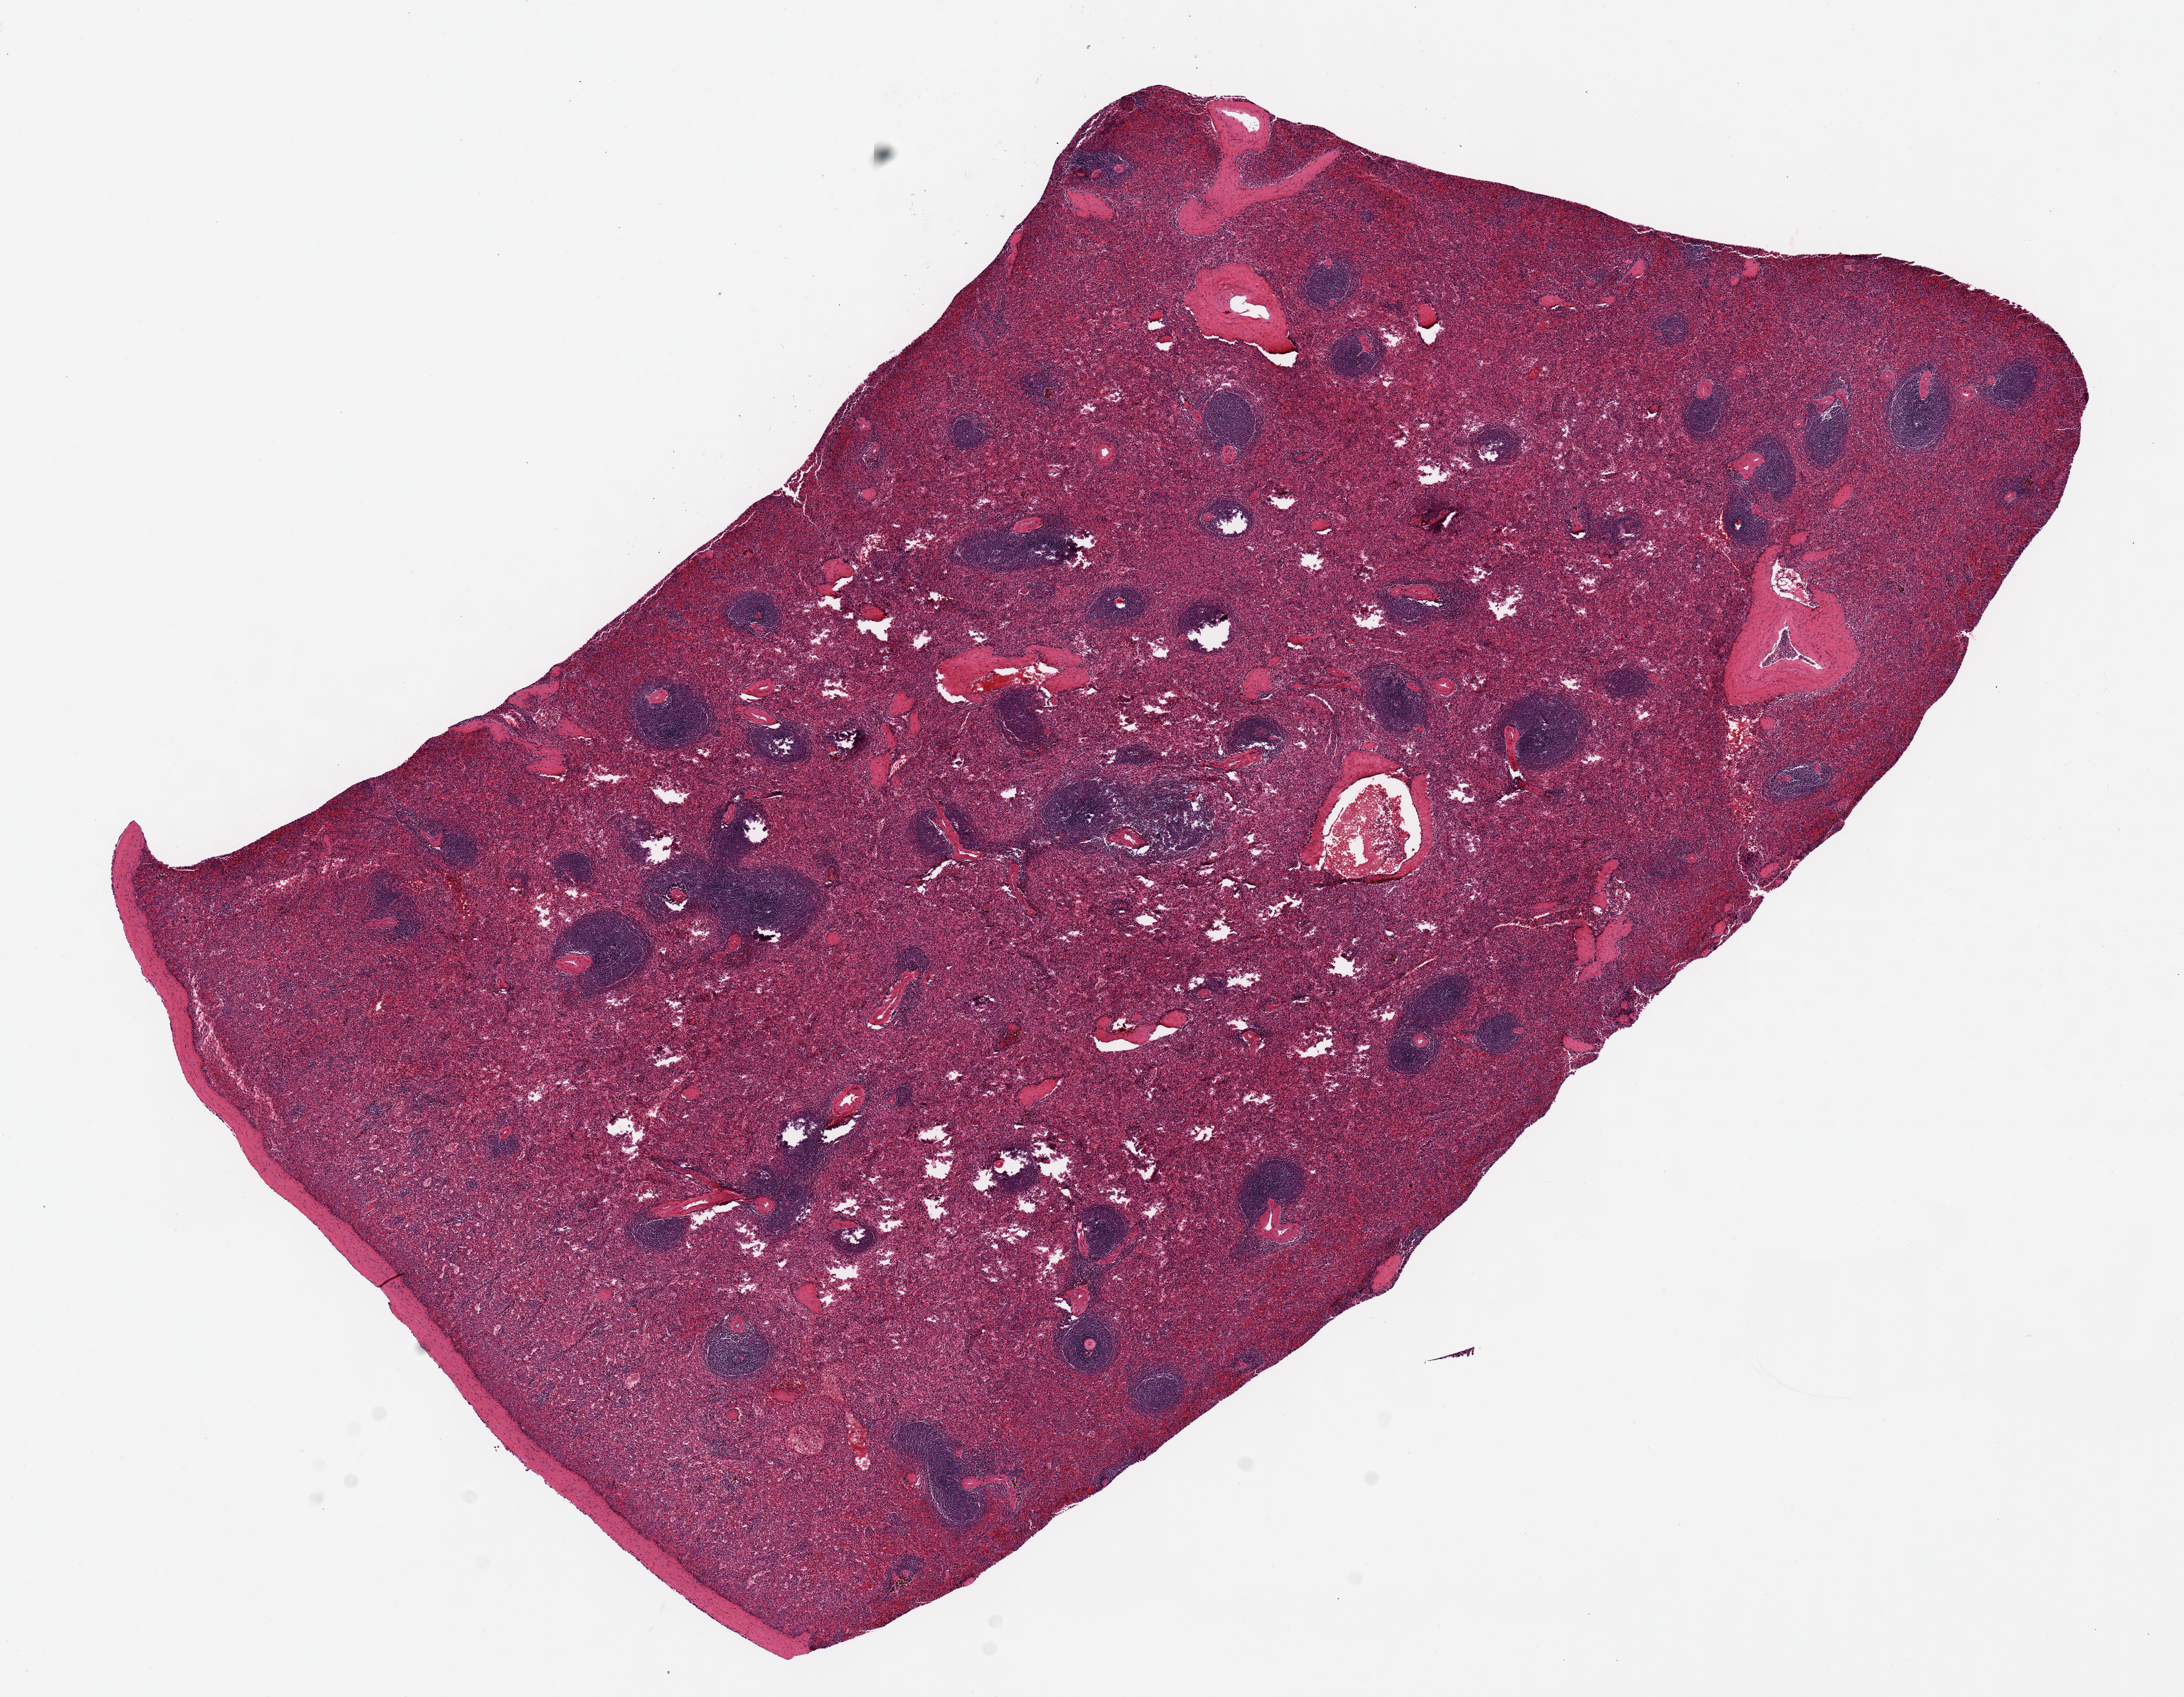
Digitized hematoxylin and eosin (H&E)-stained section, brightfield, a low-resolution overview of the entire scanned area, about 14.8 x 11.5 mm (acquisition: 20x scan), PAXgene-fixed, paraffin-embedded tissue, target tissue: spleen, tissue donor sample.
Reviewer comment on this tissue sample: Appears underfixed, many tears/holes.